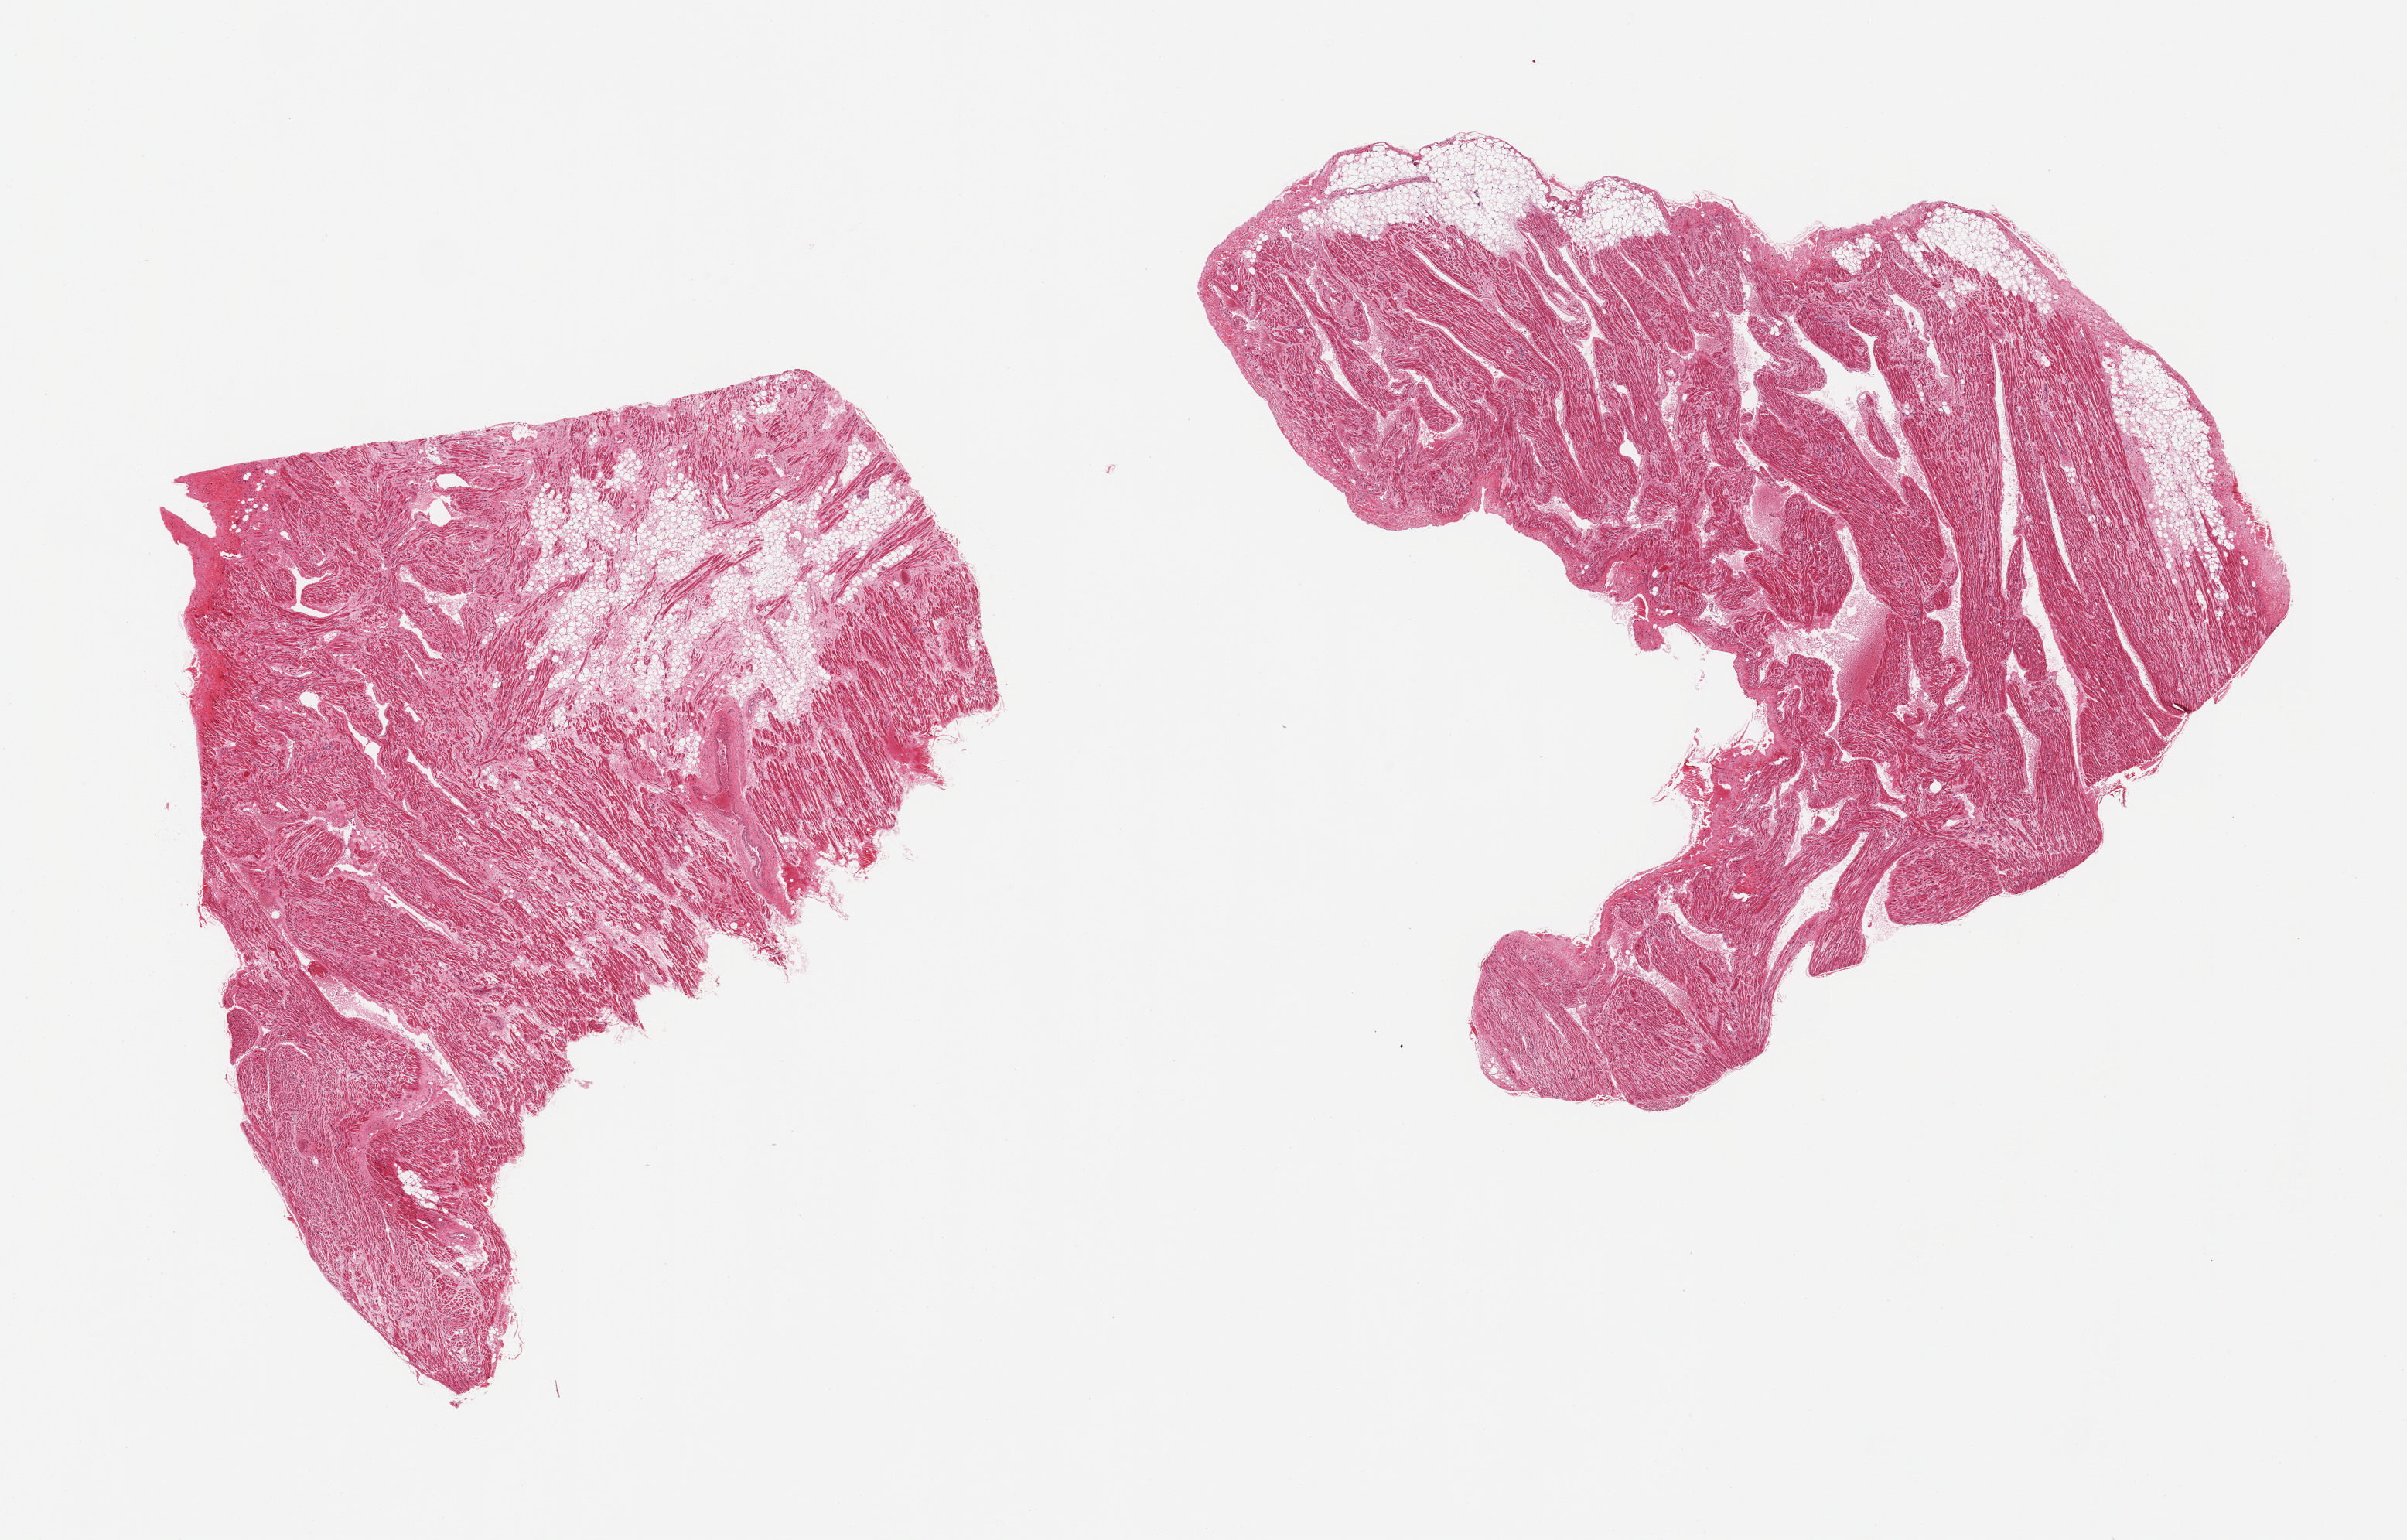
Haematoxylin and eosin whole-slide image, brightfield — whole scanned area (about 24.6 x 15.7 mm) shown as a low-resolution overview. PAXgene-fixed paraffin-embedded (PFPE) section. Sampled site (target tissue): auricular appendage. Tissue donor sample. Female donor.
Pathologist's review note for this sample: 2 pieces; 20 & 10% internal fat.